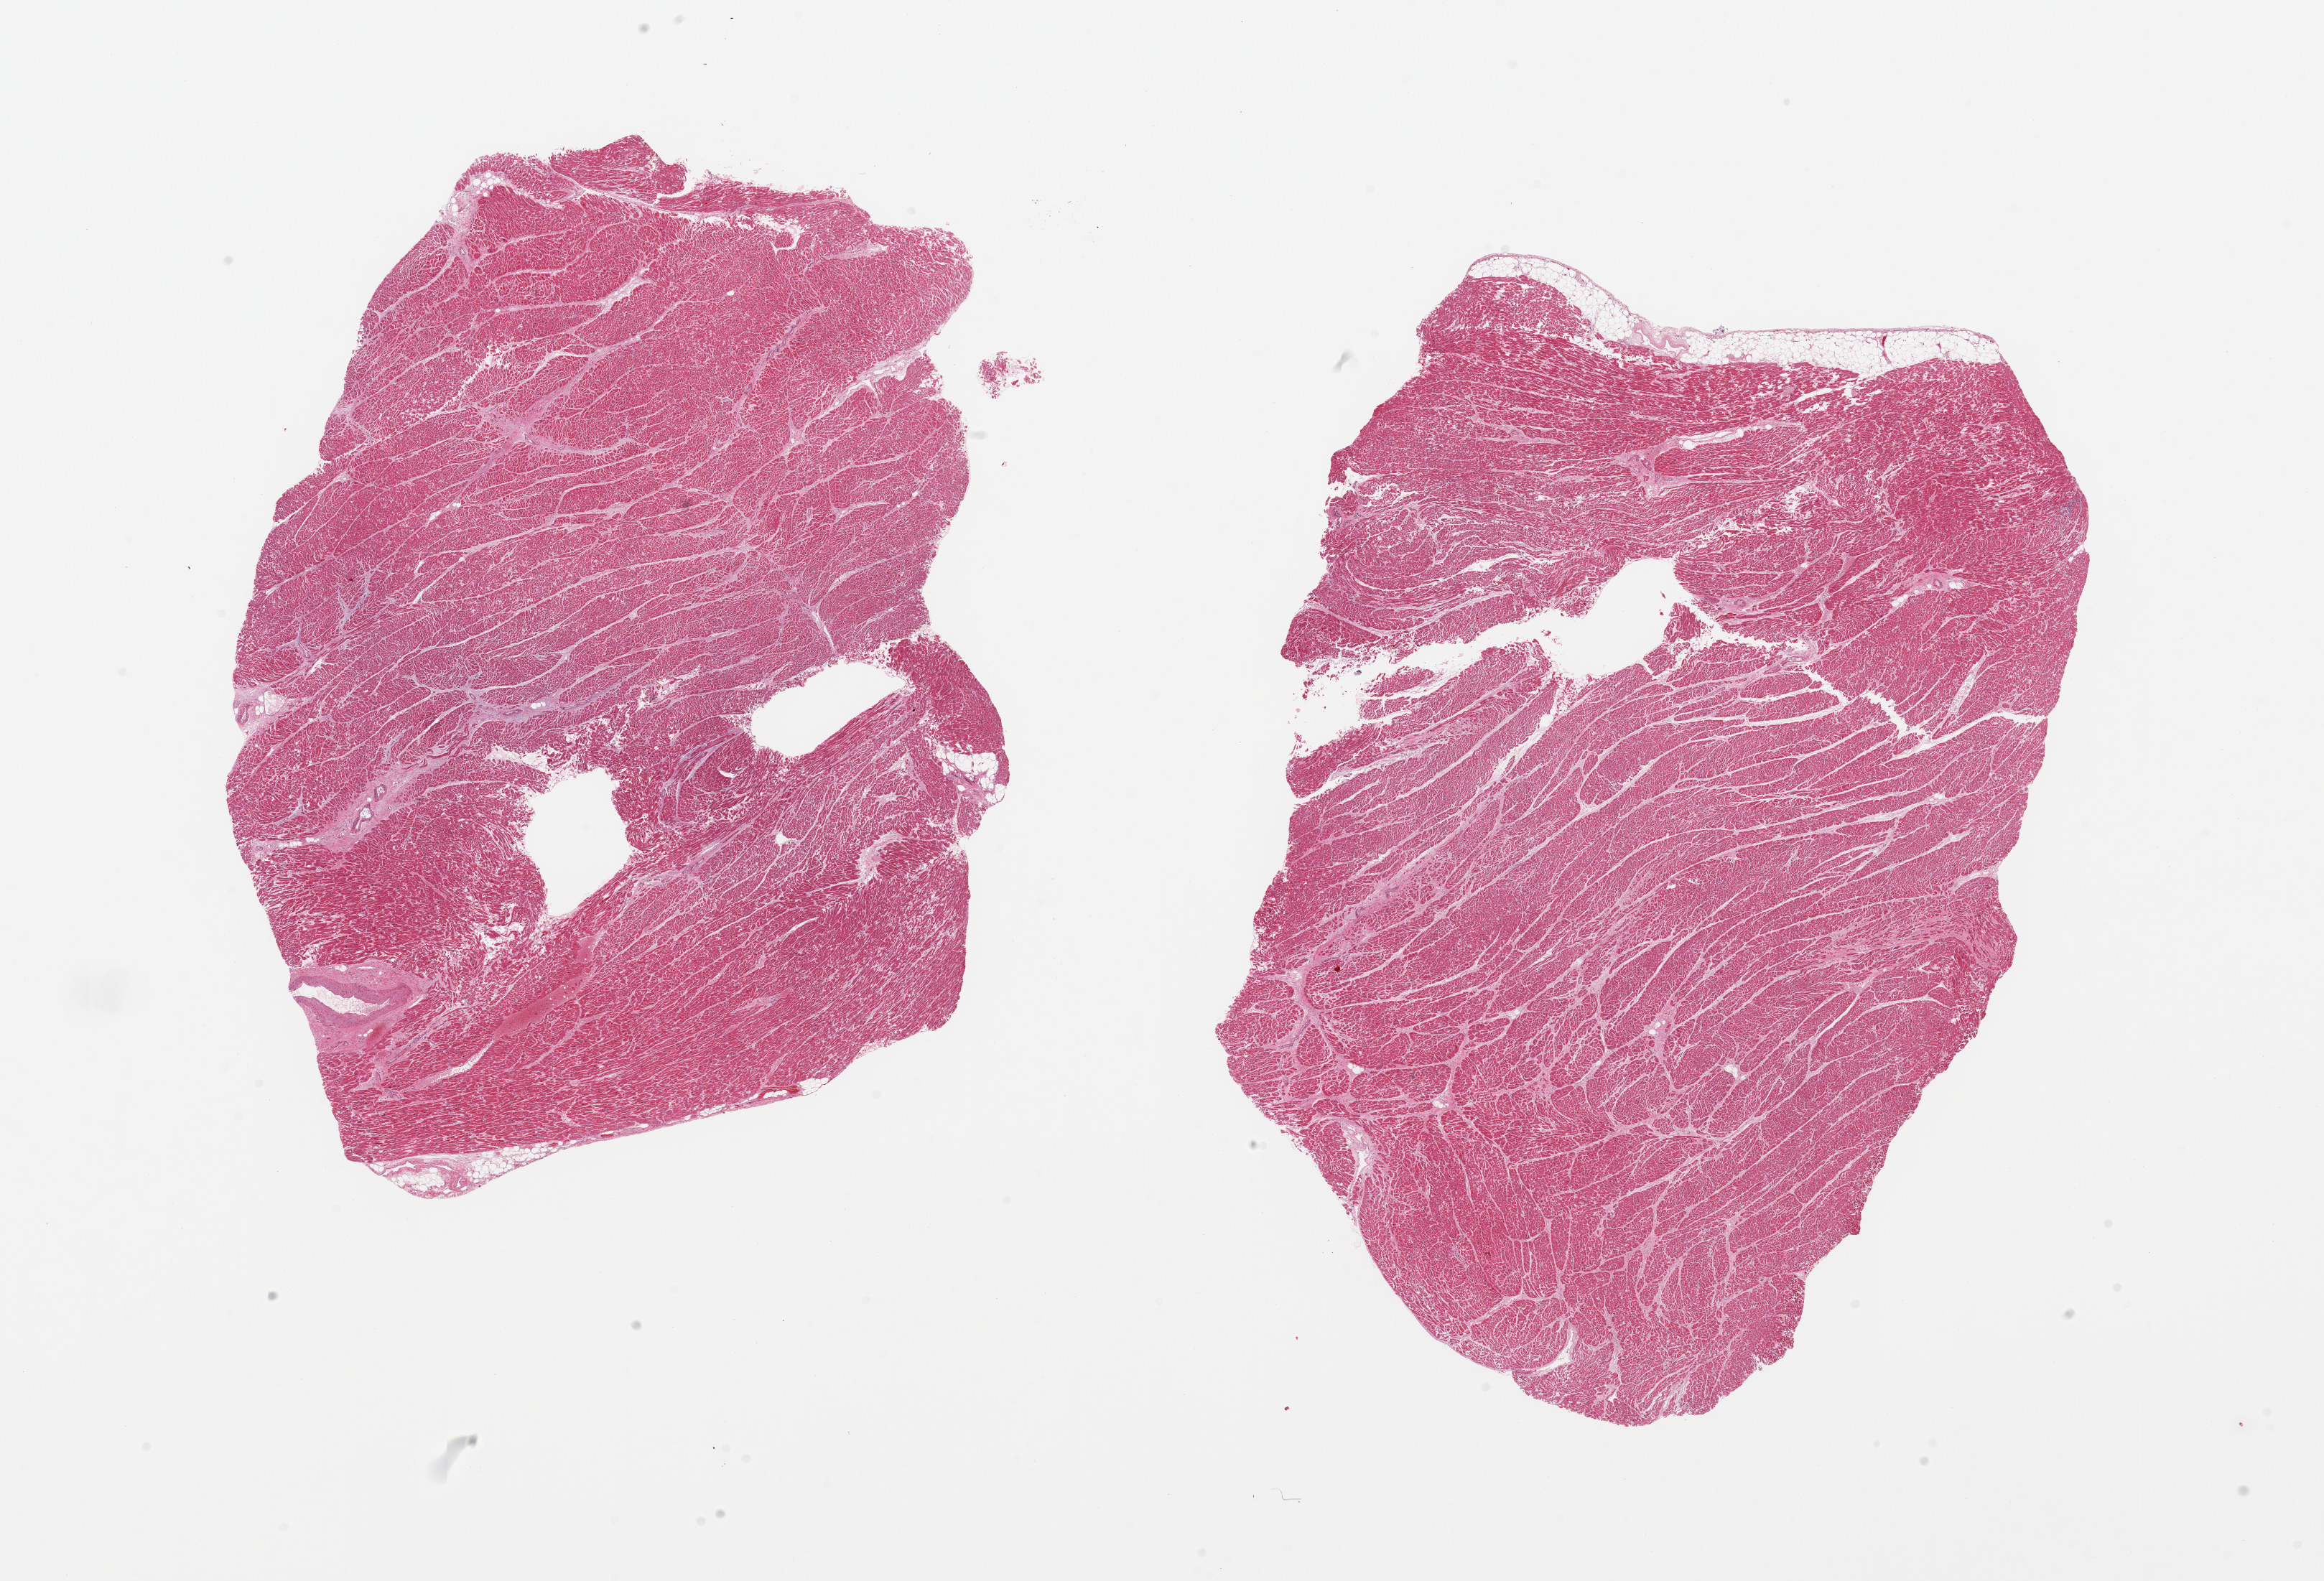
Haematoxylin and eosin whole-slide image — a low-resolution overview of the entire scanned area, about 25.6 x 17.4 mm, PAXgene-fixed, paraffin-embedded tissue, section of heart (target tissue), donor tissue sample. Male donor.
Reviewer comment on this tissue sample: 2 pieces, mild interstitial fibrosis/chronic ischemia.